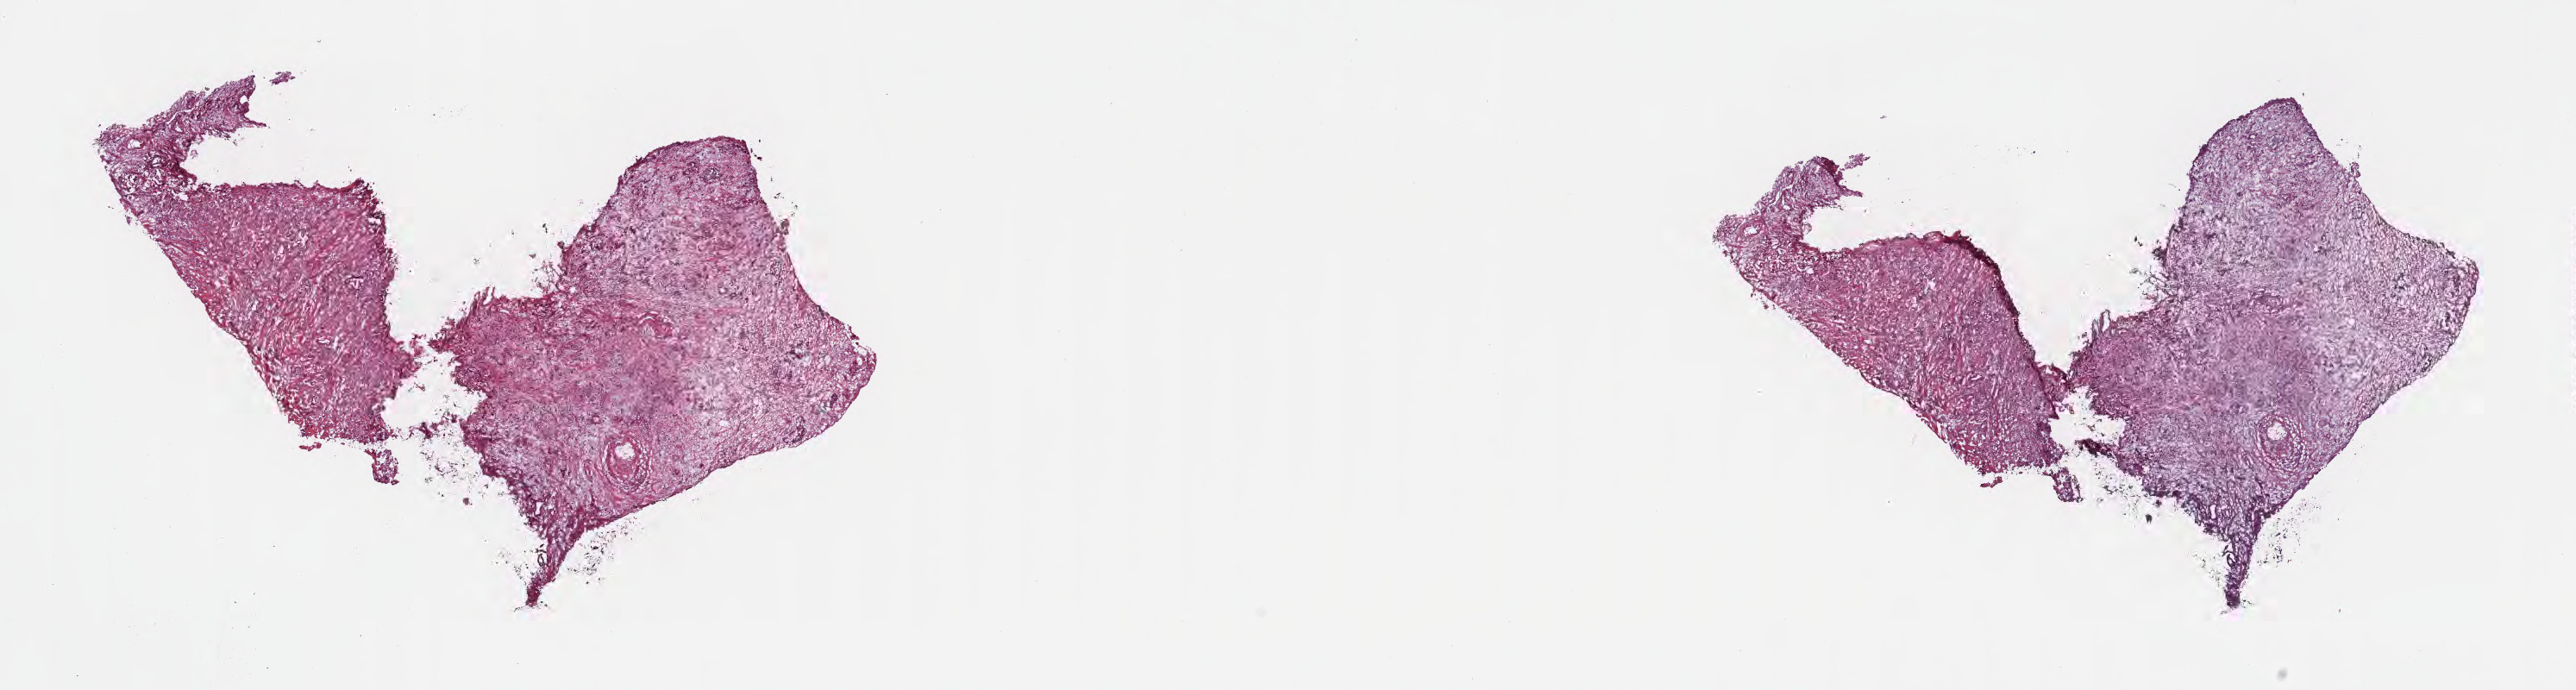
Whole-slide image, haematoxylin and eosin stain, low-resolution overview of the scanned area, about 24.2 x 6.5 mm. Frozen section. Primary tumor. Site: head of pancreas. Male, age 75 years at initial diagnosis. Tumor grade: G2 (moderately differentiated). Slide review estimates, as recorded: tumor cells 10%, tumor nuclei 80%, stromal cells 90%, necrosis 0%, normal cells 0%. Inflammatory infiltration, as recorded: lymphocyte infiltration 0%, monocyte infiltration 0%, neutrophil infiltration 0%.
Histologic diagnosis: Infiltrating duct carcinoma, NOS. Section: bottom of the tissue portion. AJCC pathologic stage: Stage III.